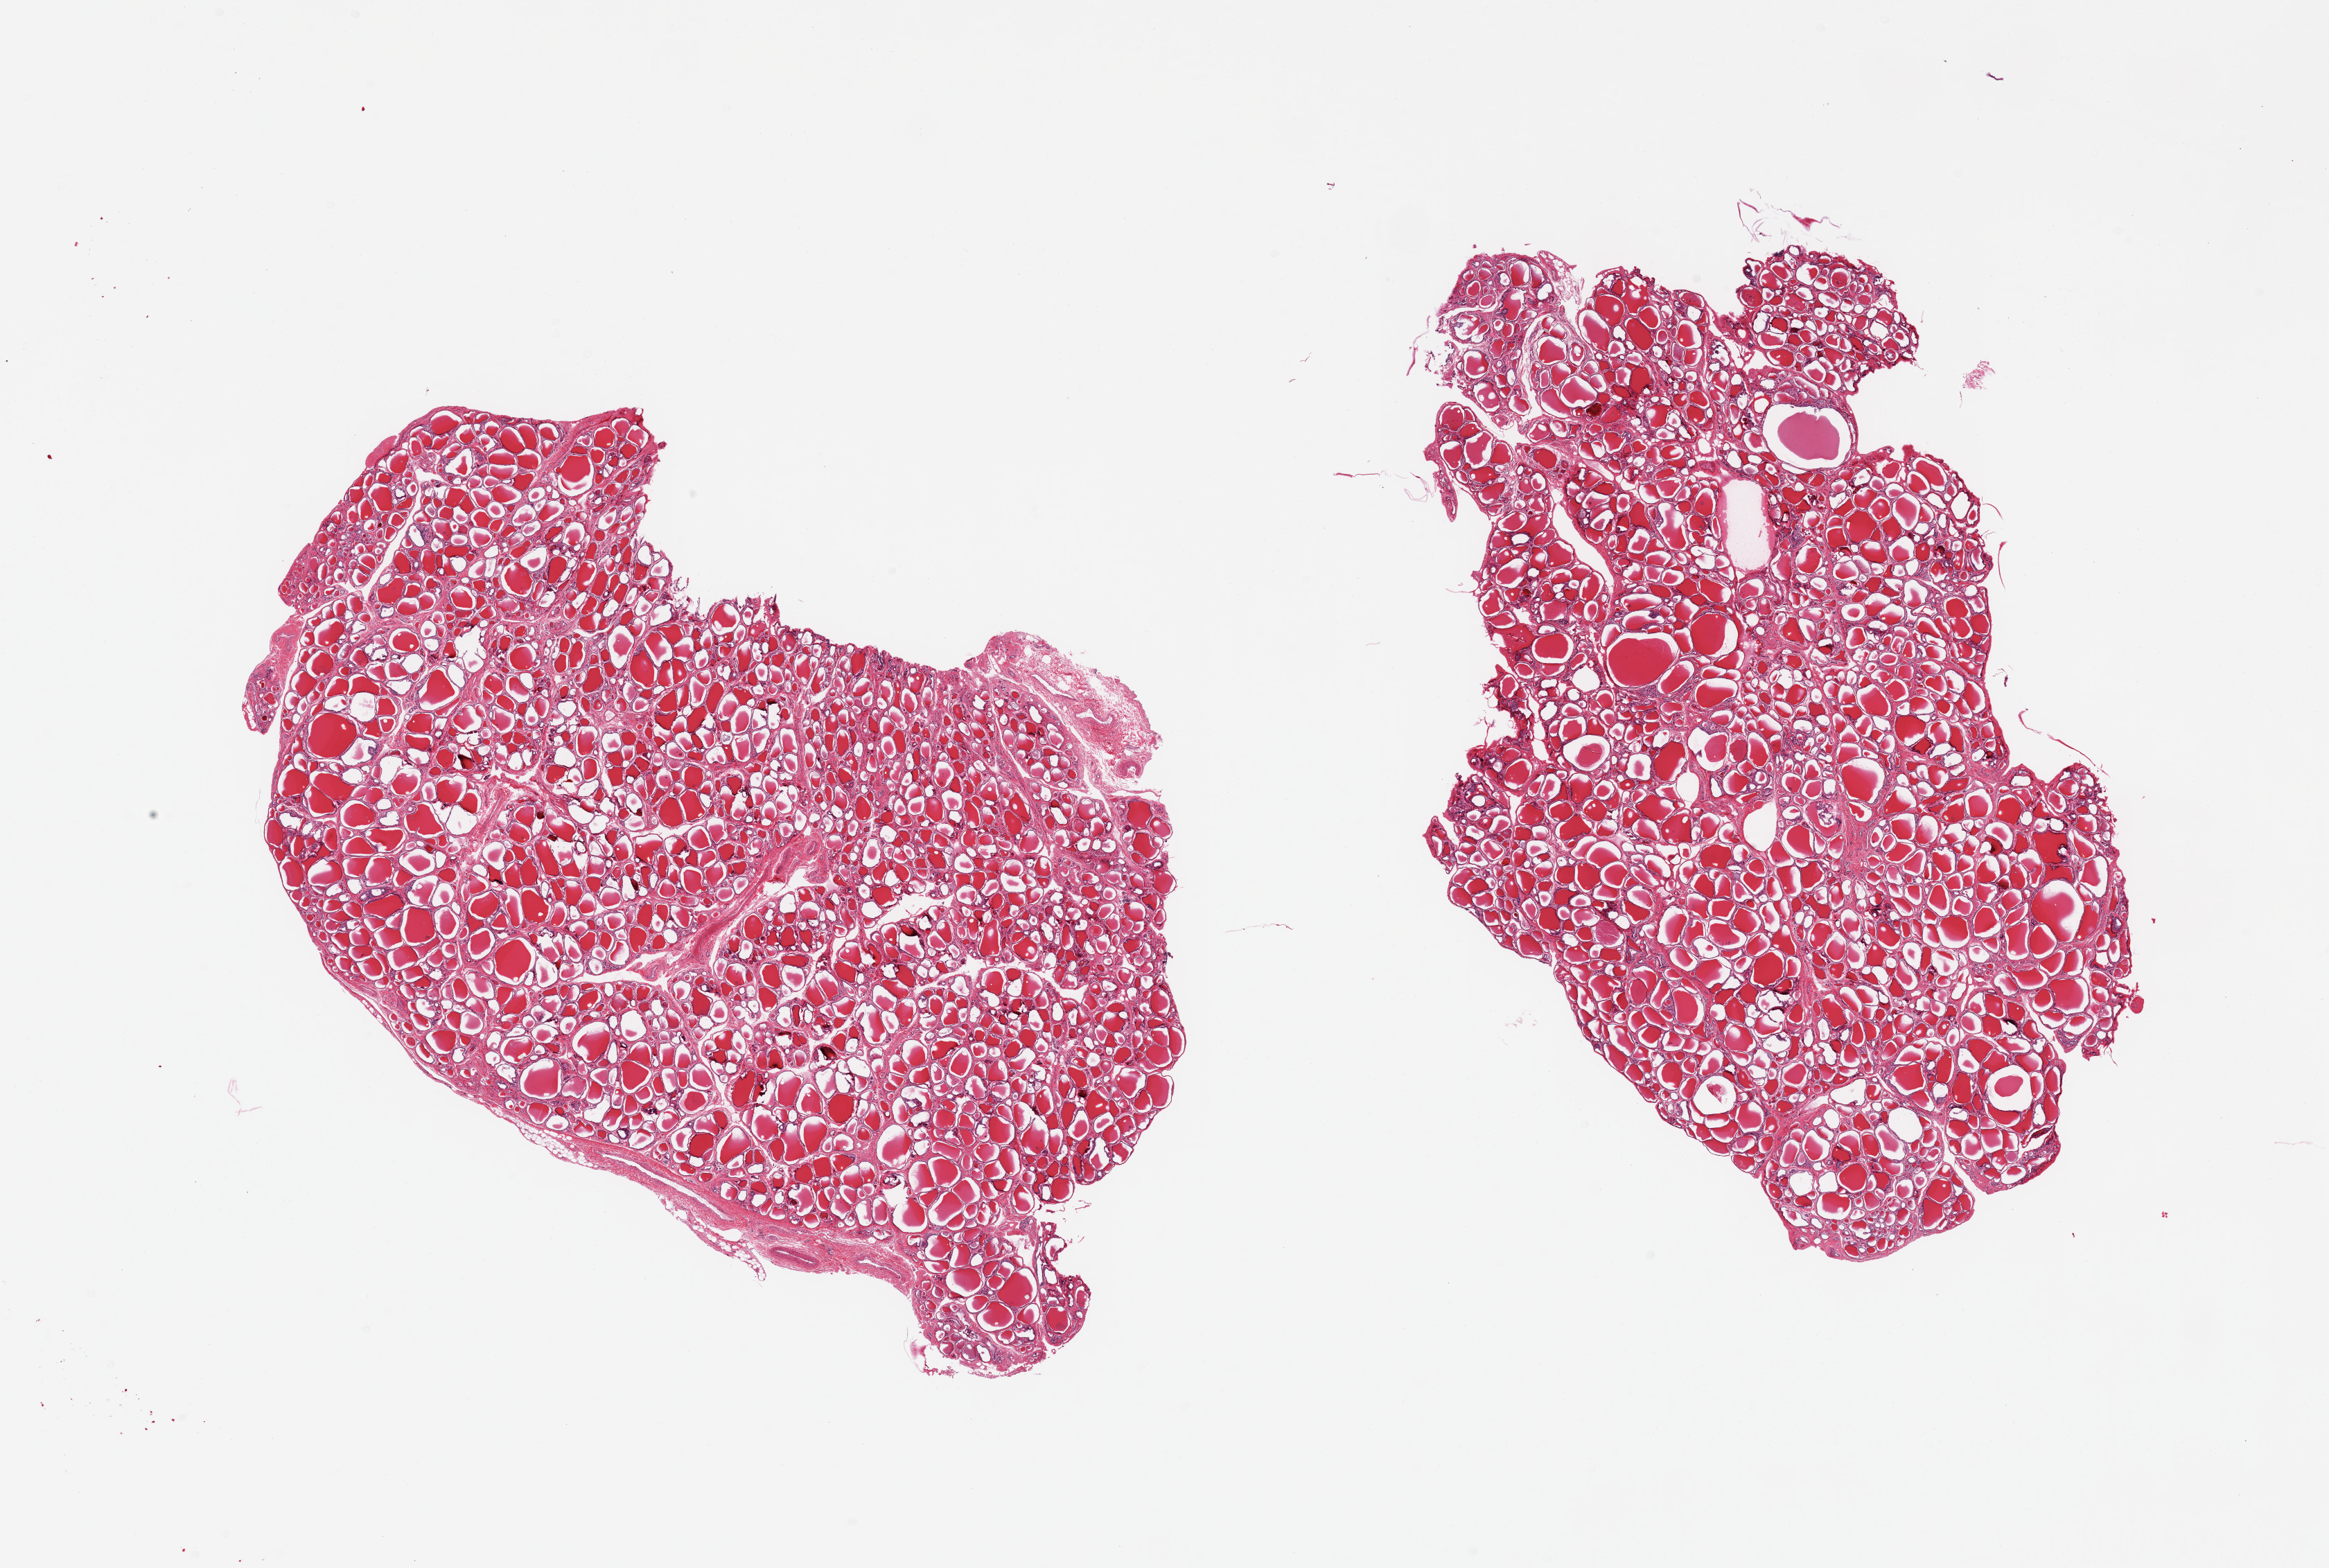
Digitized haematoxylin and eosin-stained section, brightfield — a low-resolution overview of the entire scanned area, about 26.6 x 17.9 mm, PAXgene-fixed, paraffin-embedded tissue, sampled site (target tissue): thyroid, donor tissue sample. Male donor.
Reviewer comment on this tissue sample: 2 pieces; unremarkable.